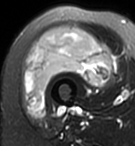
MRI of an extremity soft-tissue mass, one axial slice. Position 36 of 95 along the scan axis. T2-weighted fat-saturated. MR volume resampled by the dataset authors to the PET/CT grid (not the native acquisition matrix). 135 × 146 image matrix. Female patient. Case-level facts recorded for this patient, not image findings: histological type: pleiomorphic undifferentiated sarcoma; grade: high; site of the primary tumour: right quadricep.
Annotated regions visible in this slice (expert contour drawn on MRI and transferred to this co-registered scan by the dataset authors):
- gross tumour volume including surrounding oedema: bounding box <25,27,111,114> (left, top, right, bottom; pixels)
- gross tumour volume (mass): <25,27,111,114>